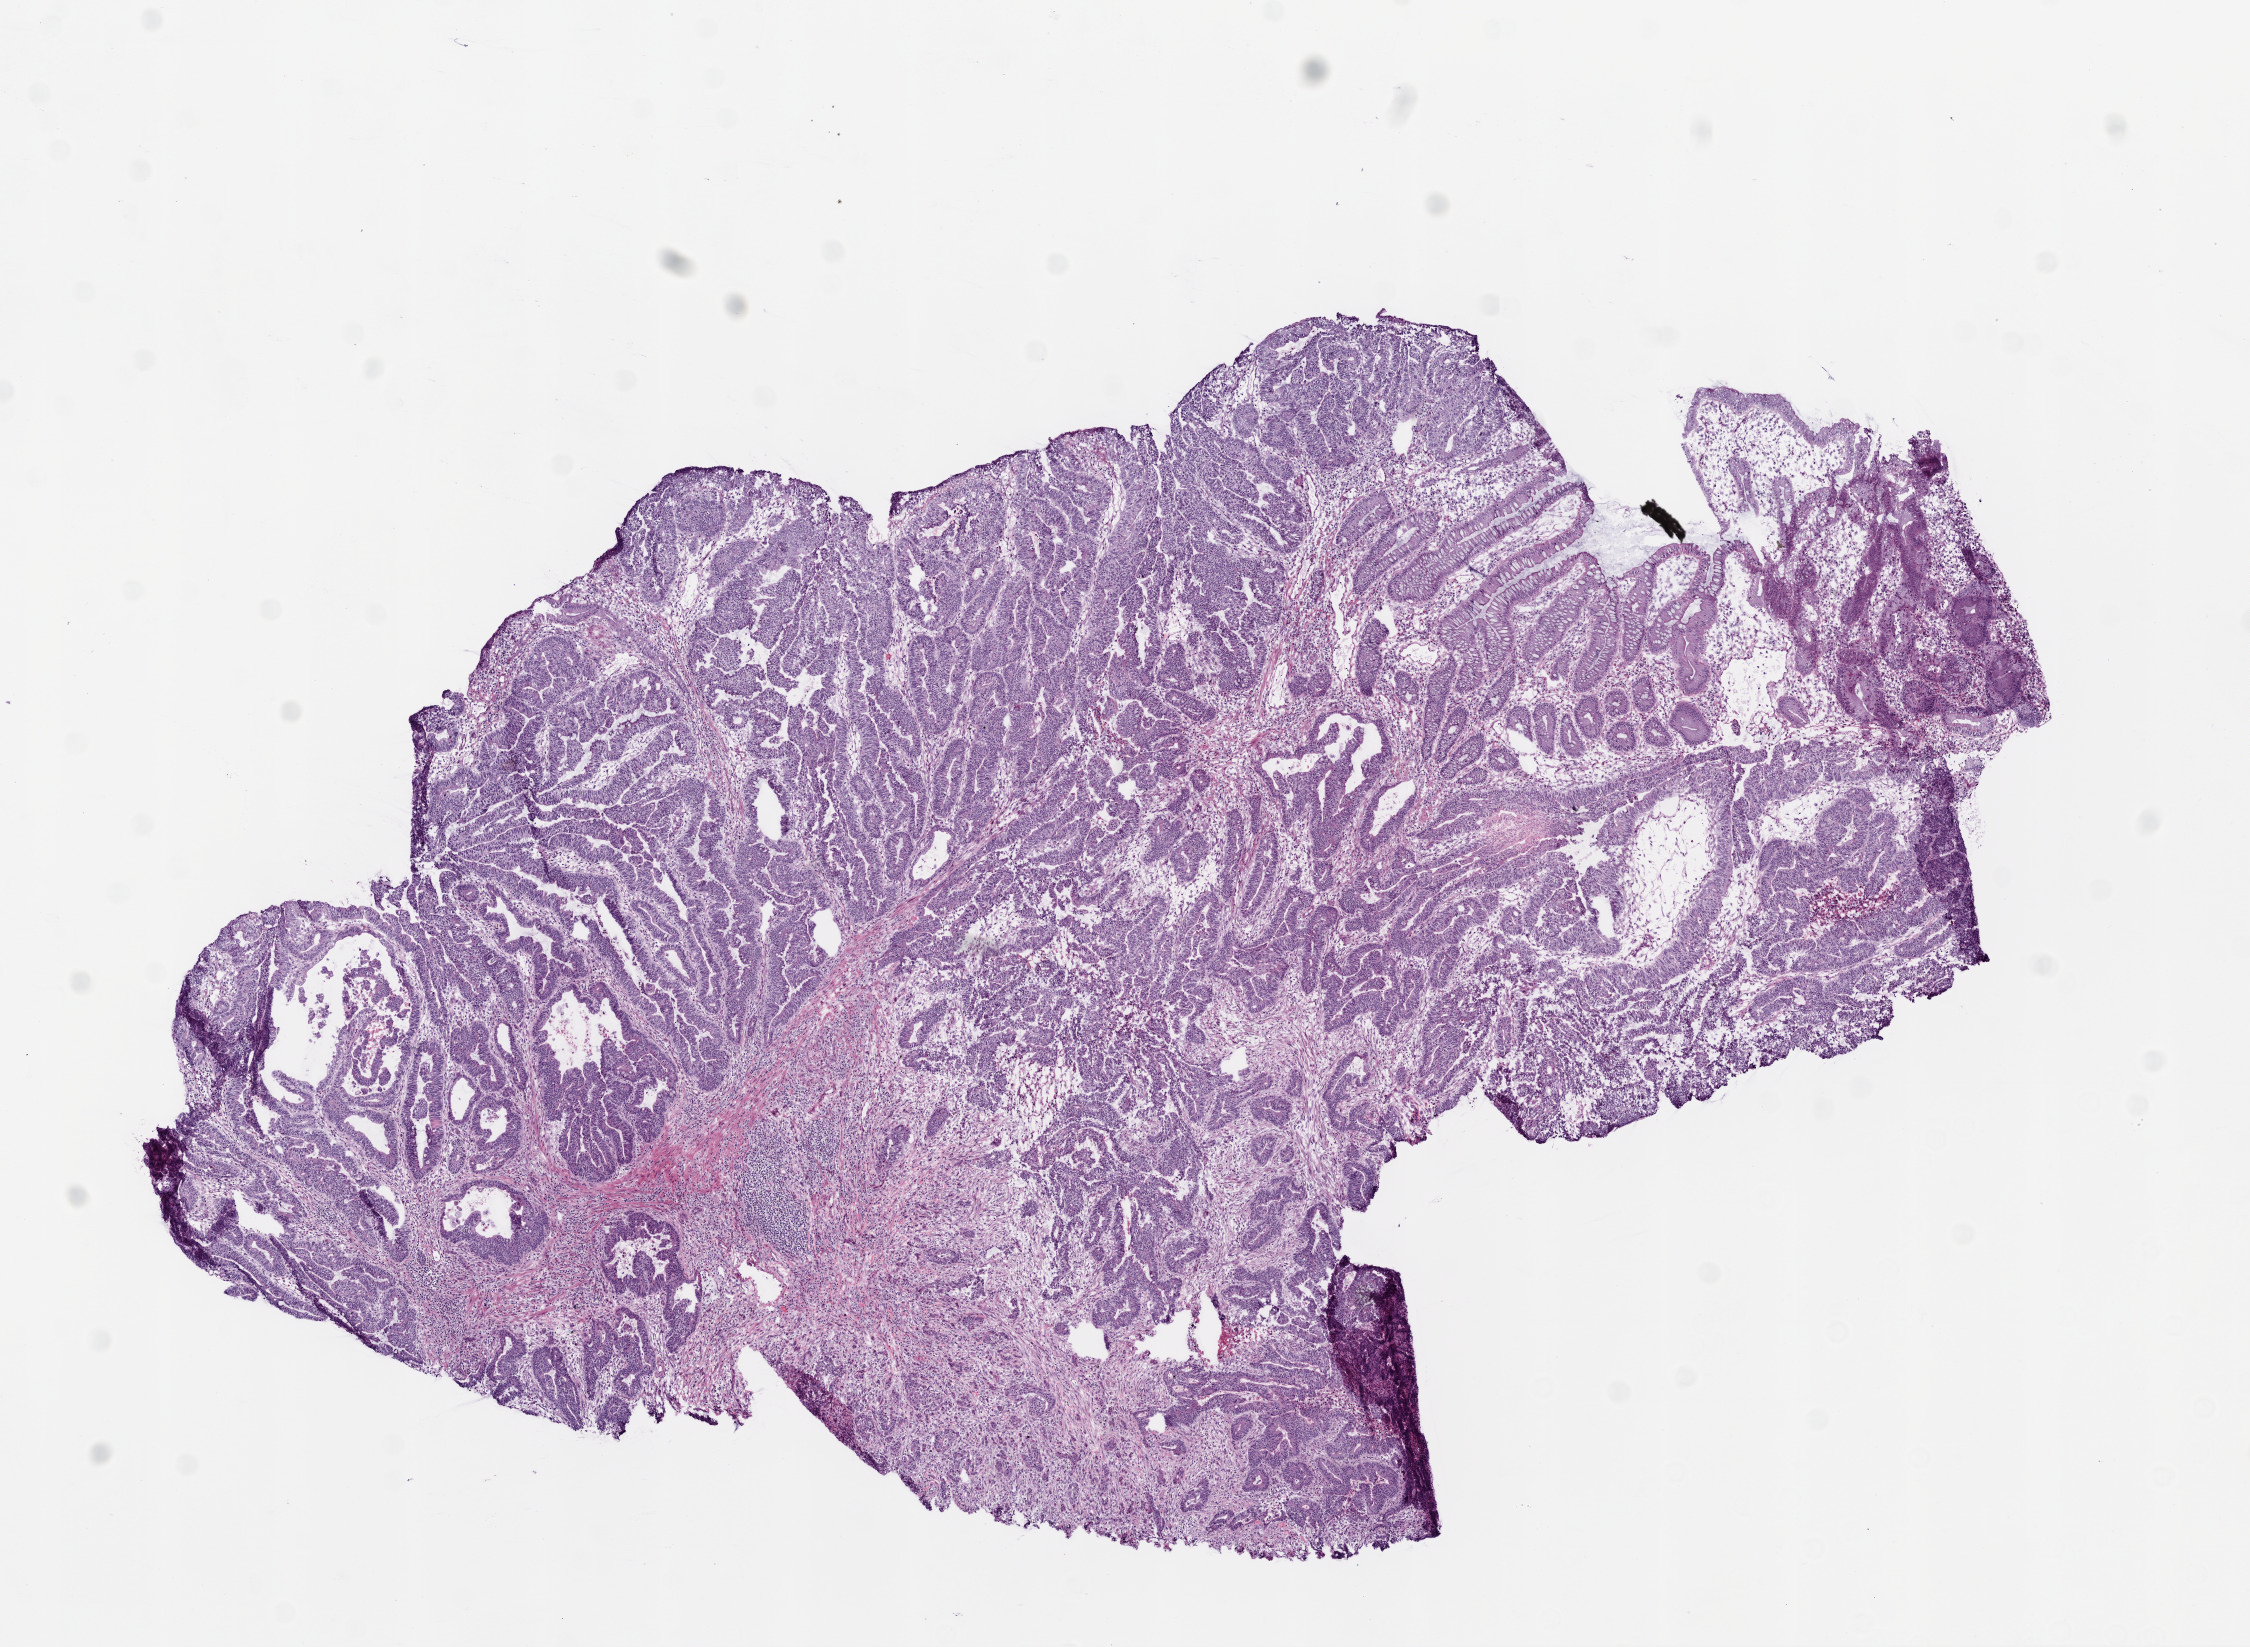
Whole-slide histology image, H&E, low-resolution overview of the scanned area, about 9.0 x 6.6 mm, frozen section from the top of the tissue portion, rectum, primary tumour sample. Patient: female, age at initial diagnosis 78 years. Pathologist review of this section (percent, as recorded): tumour cells 73%, tumour nuclei 65%.
Pathologic diagnosis: Adenocarcinoma, NOS (rectosigmoid junction).